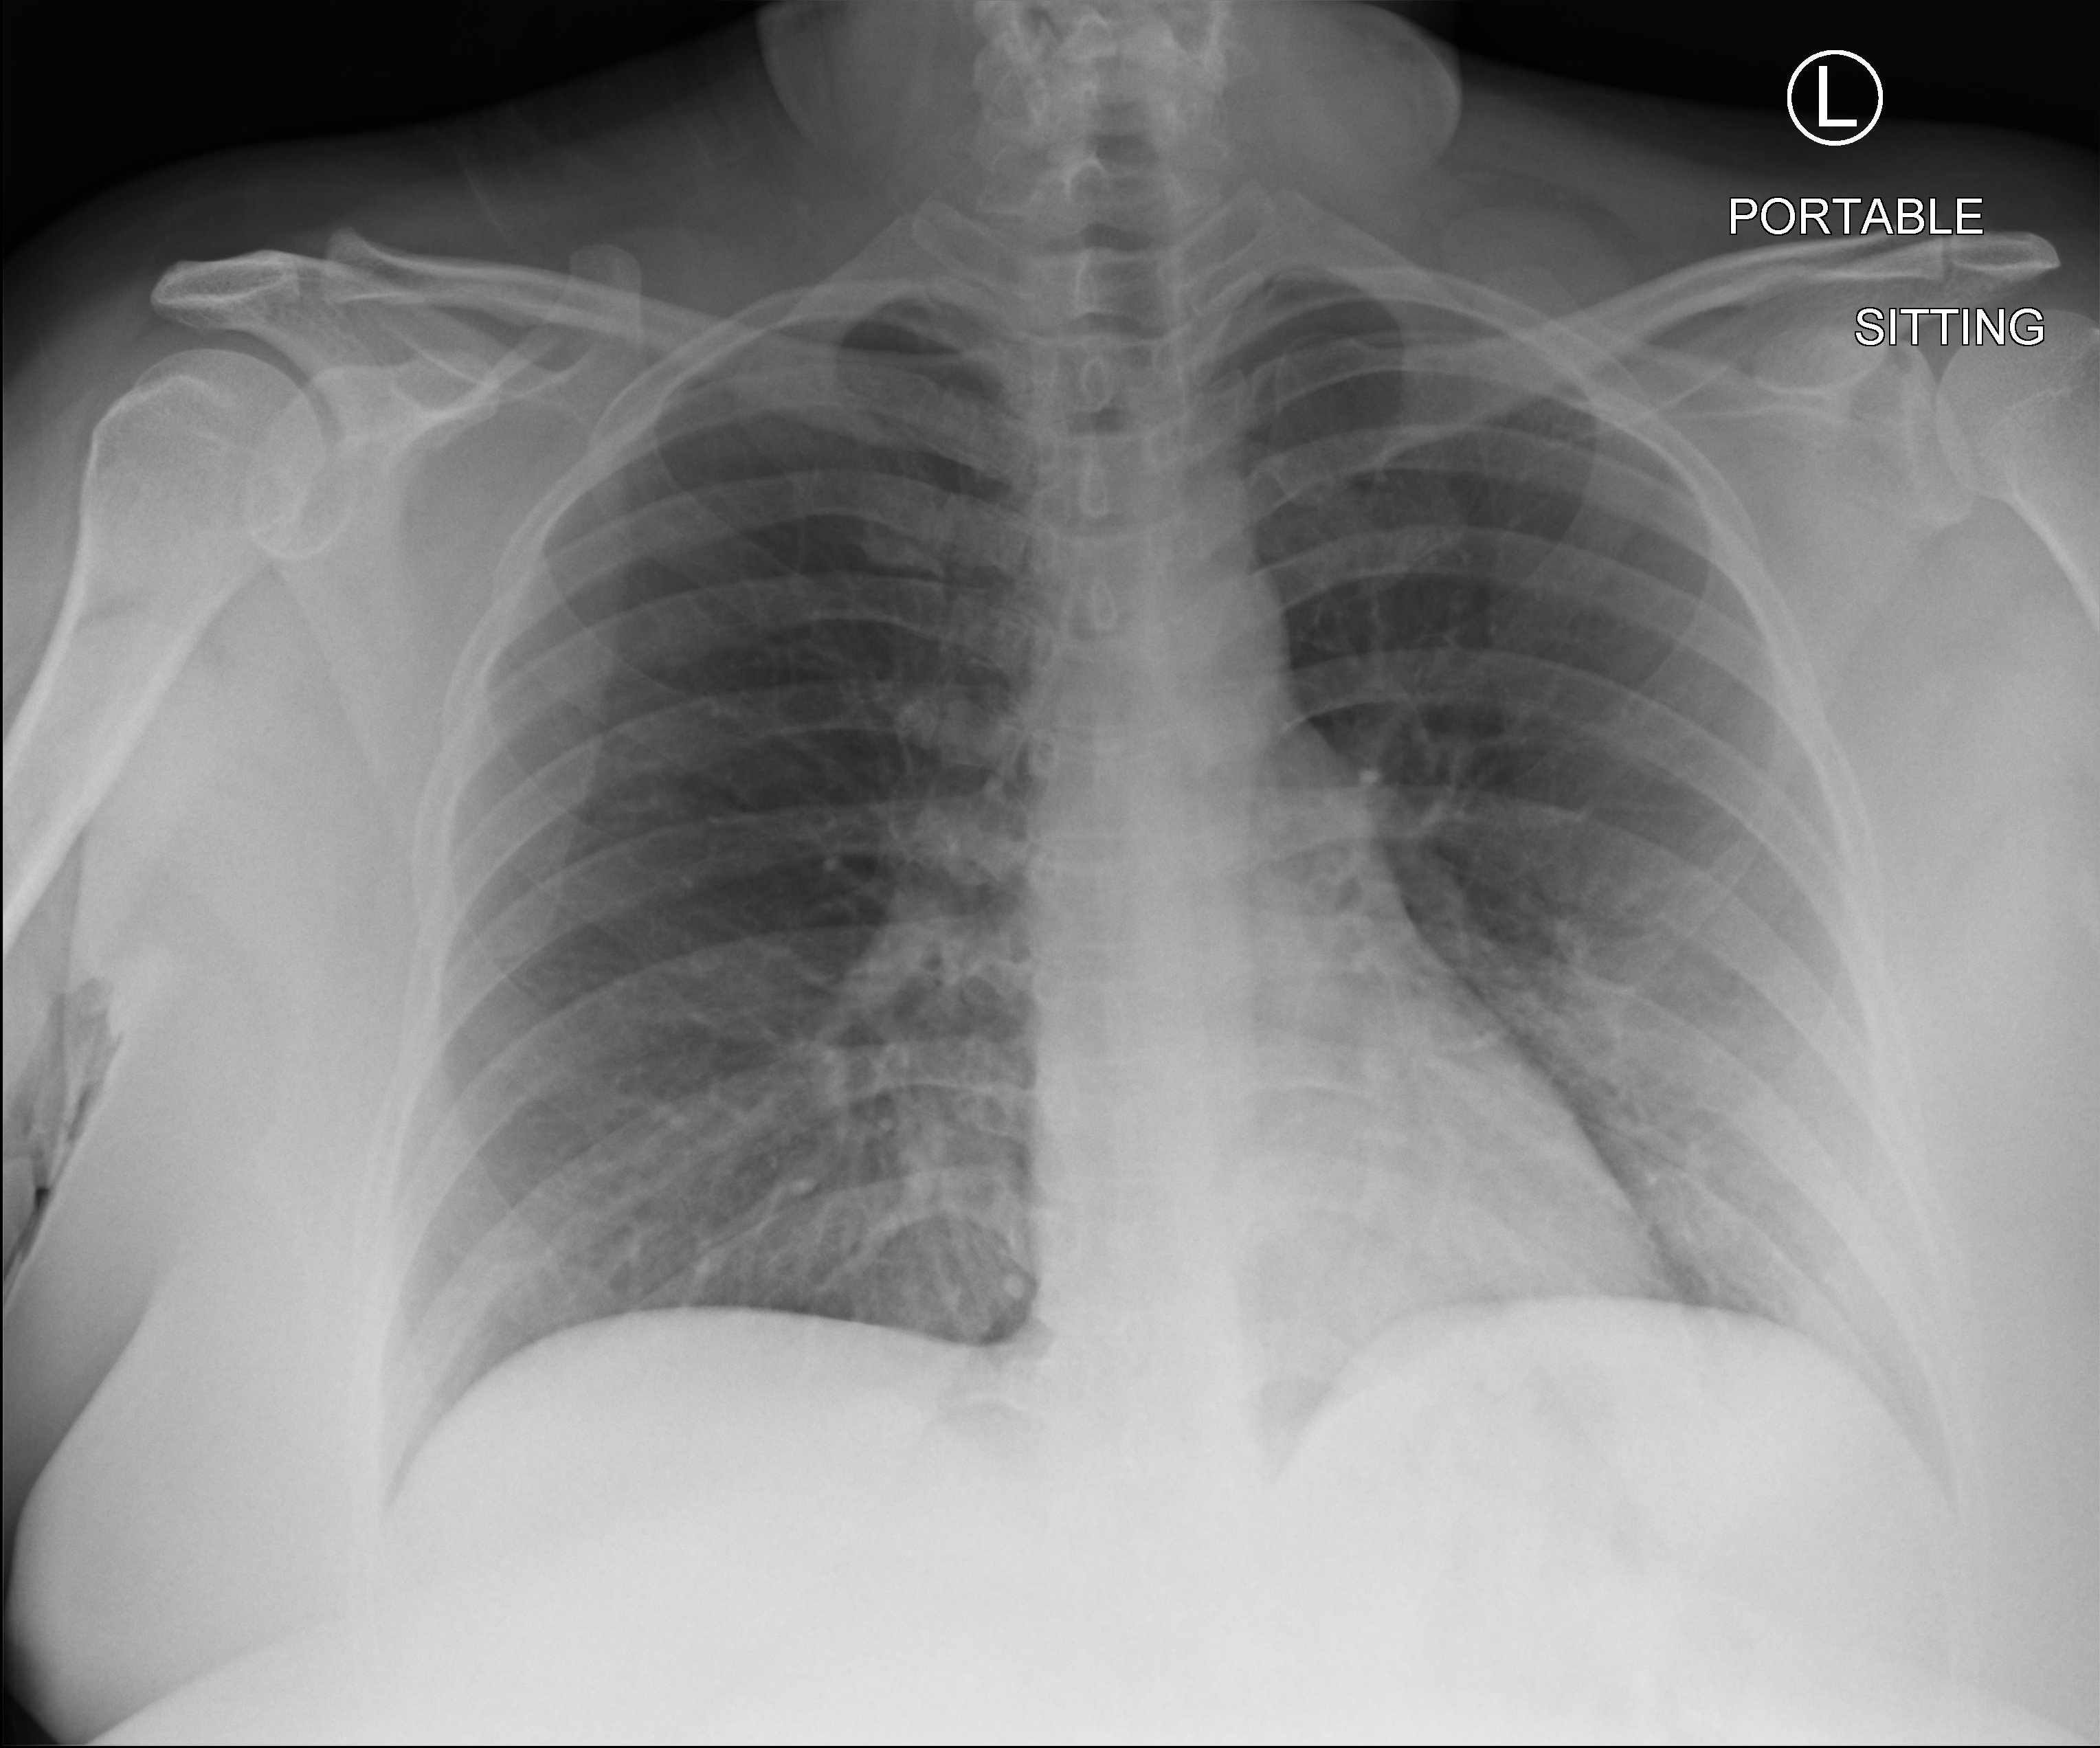
Bedside chest radiograph (computed radiography), anteroposterior (AP) projection. Female patient hospitalised with COVID-19, age 18–59 years.
Admission-level facts for this patient (not findings on this image; timing relative to this image not recorded):
- admitted to intensive care during this hospital stay: no
- mechanically ventilated during this hospital stay: no